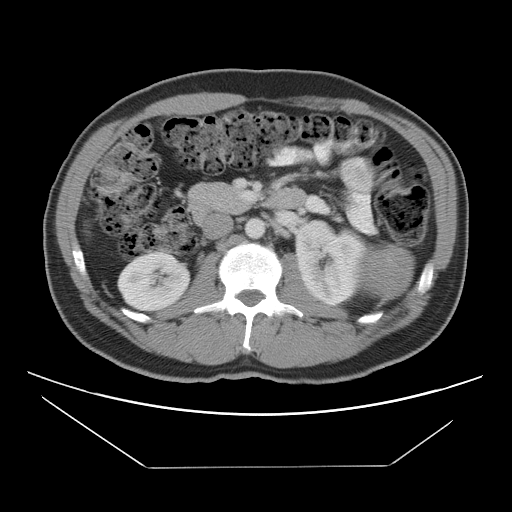
Contrast-enhanced abdominal CT, one axial slice. Intravenous contrast given. Soft-tissue window (W 400 / L 40 HU). 5 mm slice thickness. 512 × 512 image matrix, field of view 396 × 396 mm. Patient: male, 44 years. From the clinical record (not read from this slice): diagnosis: adrenocortical carcinoma; tumour side: left adrenal; tumour size at pathology: 15.5 cm; Ki-67 index: 6 %.
Outlined on this slice (semi-automatic segmentation, software-assisted and operator-edited):
- mass: bounding box [x1, y1, x2, y2] px = [361, 245, 413, 298]